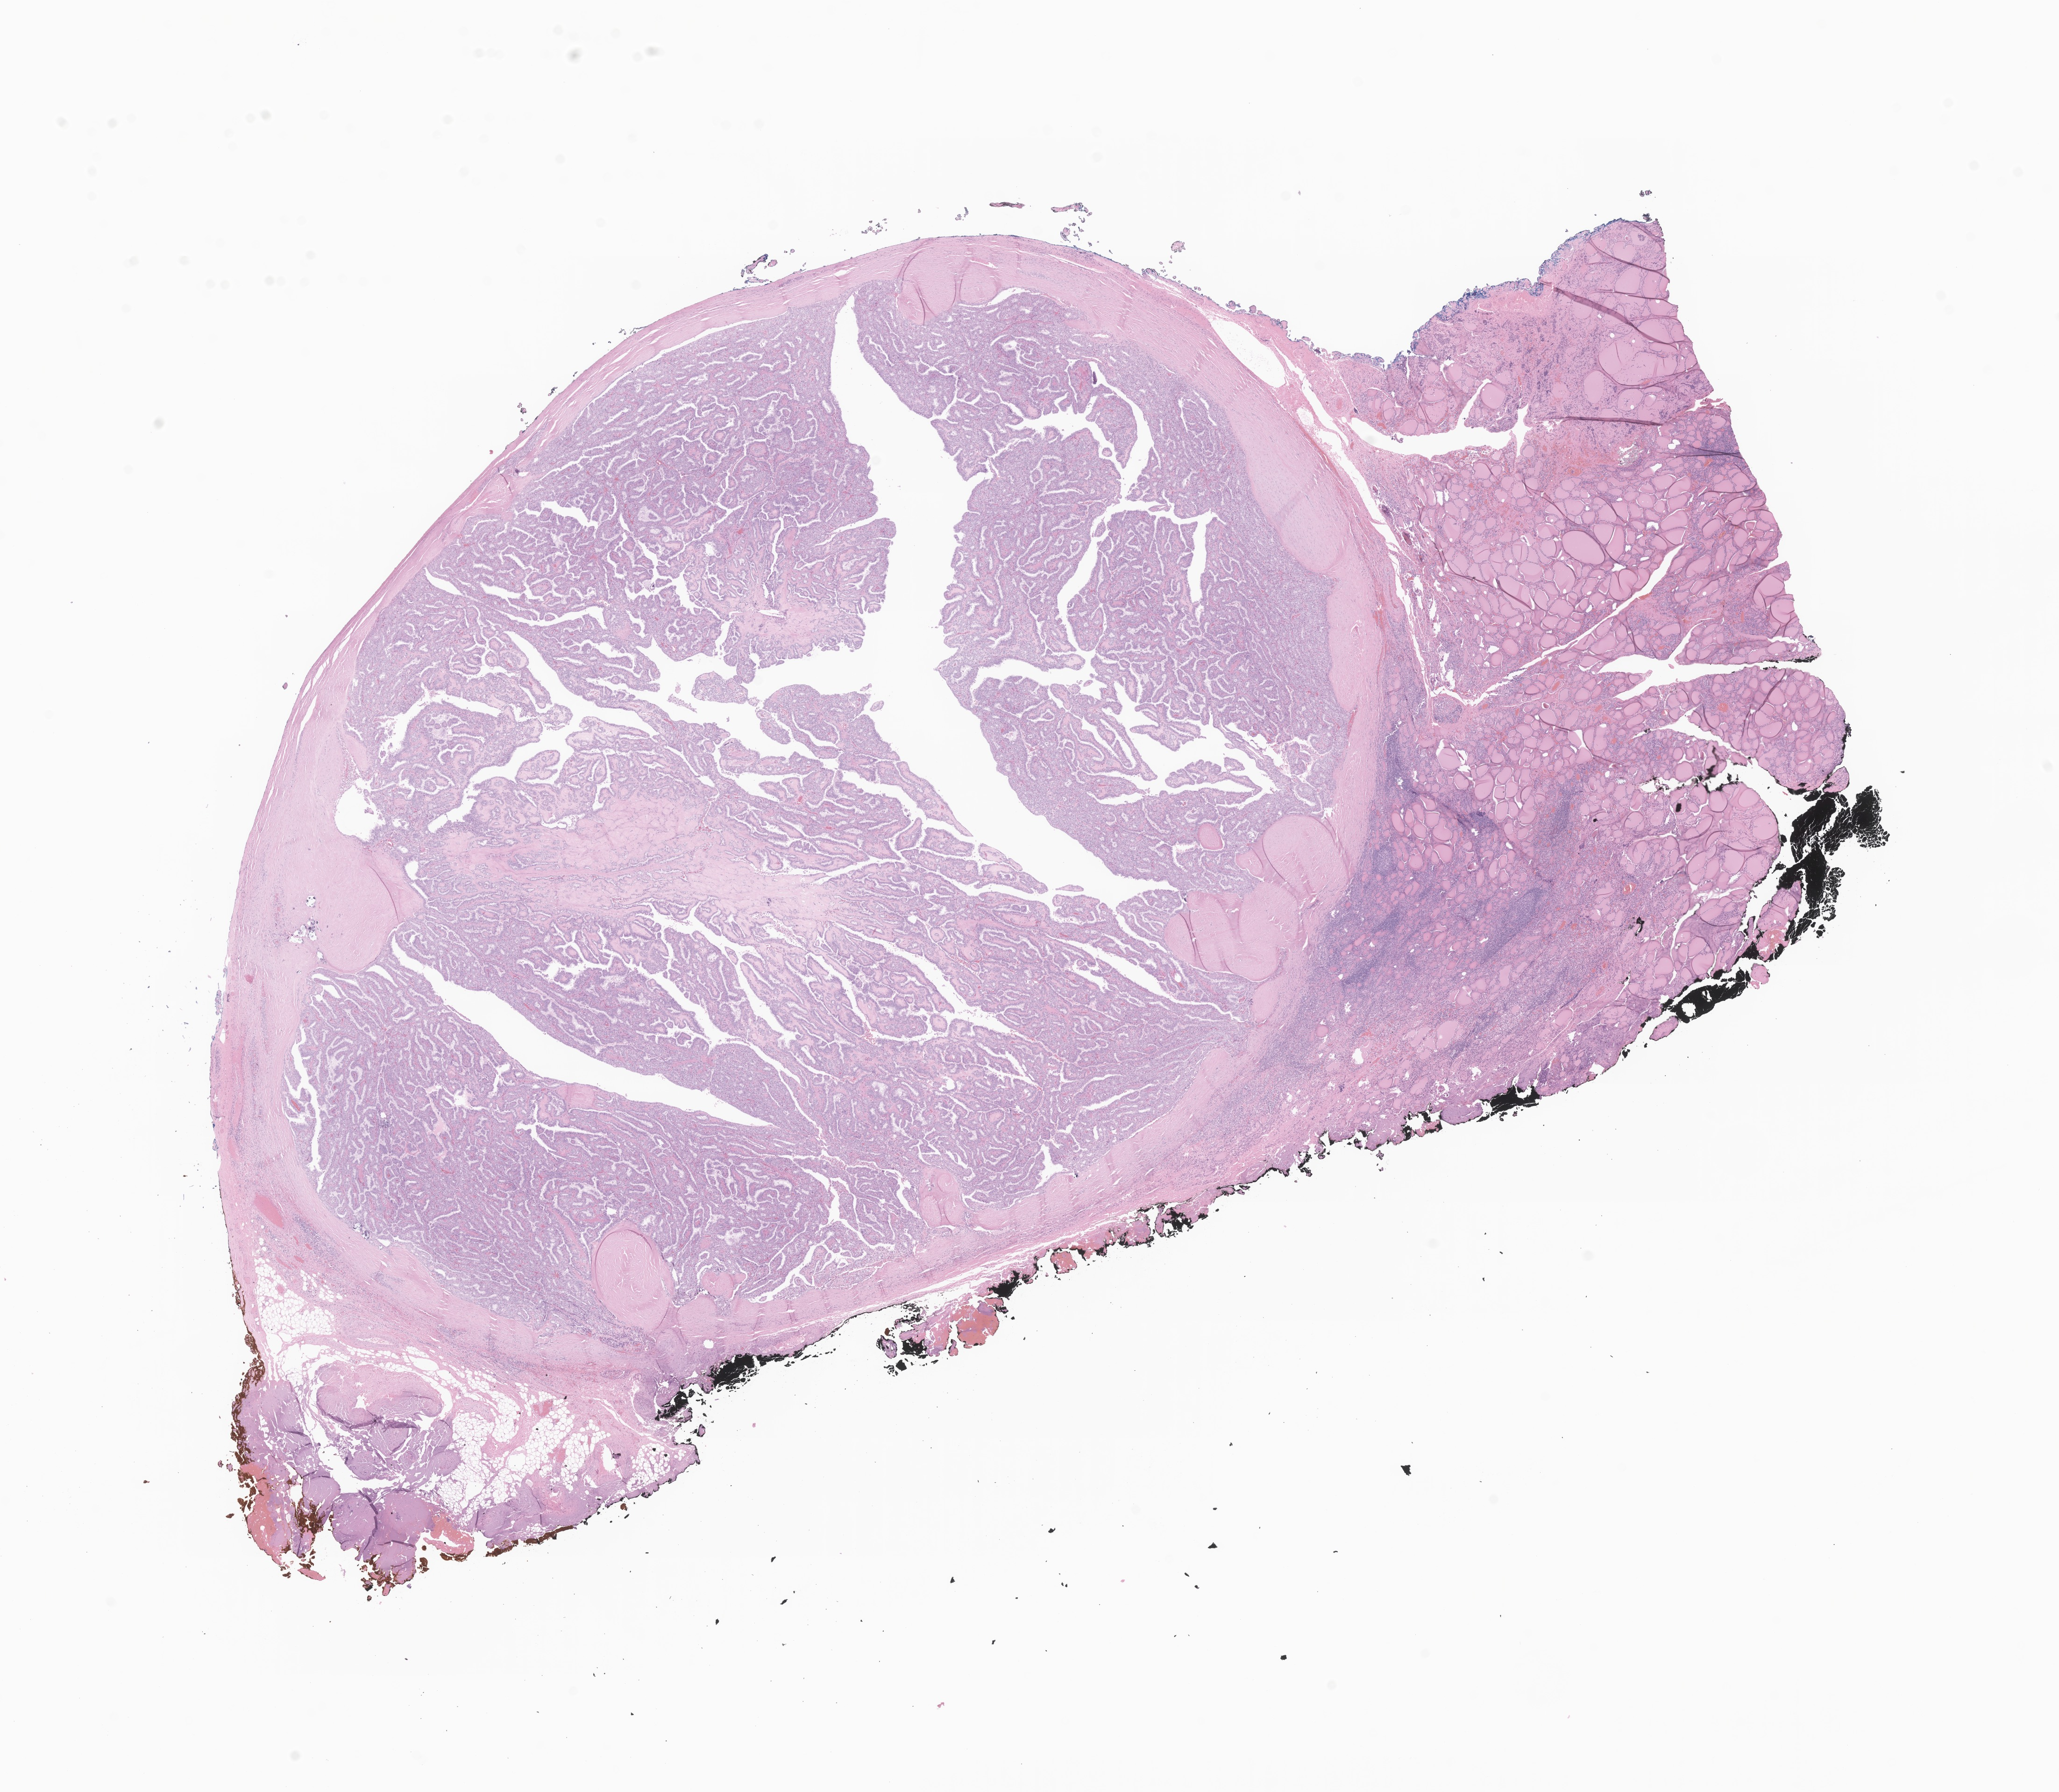
Whole-slide image, haematoxylin and eosin stain of tumor tissue from the thyroid, whole scanned area (about 18.6 x 16.2 mm) shown as a low-resolution overview. Formalin-fixed paraffin-embedded section. Patient: female, age 179 months (14 years 11 months).
Recorded diagnosis: Papillary carcinoma, NOS.